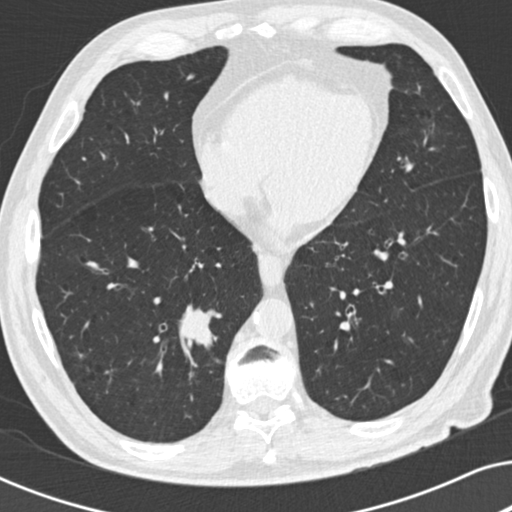
Chest CT (low-dose screening protocol), one axial image; baseline screening round; lung window (W 1500 / L -600 HU); slice 109 of 191 in the series; 512 × 512 image matrix, field of view 330 × 330 mm. Male, age 73 years at enrolment. Current smoker at enrolment.
Lesion marked by an expert reader, bounding box <159,296,225,365> (left, top, right, bottom; pixels). The screening reader recorded 2 non-calcified nodules or masses ≥4 mm on this exam (right lower lobe, right upper lobe); which of them this box marks is not recorded. Later outcome: lung cancer diagnosed 63 days after this screen — carcinoid tumor, NOS, right lower lobe, carcinoid, stage not assessed, 12 mm at pathology.